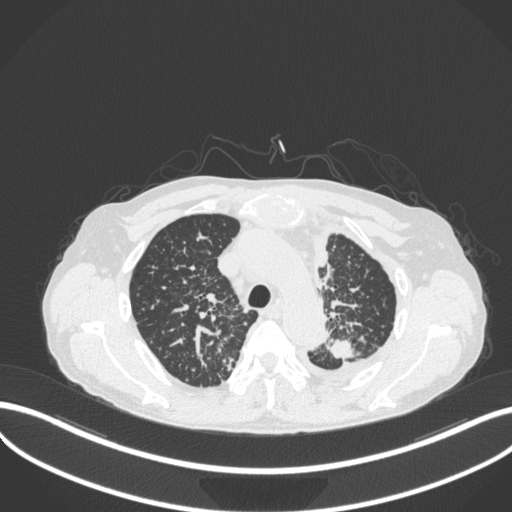
Chest CT, one axial slice; reconstruction kernel B31f; lung window (W 1500 / L -600 HU); 1 mm slice thickness; 512 × 512 image matrix, field of view 400 × 400 mm. Male patient, age 58 years. Case-level facts recorded for this patient, not image findings: clinical TNM (as recorded): T1c N3 M1.
Outlined on this slice (bounding box drawn by a radiologist):
- lung tumour (recorded histology: adenocarcinoma): box from (x=328, y=336) to (x=362, y=361) px